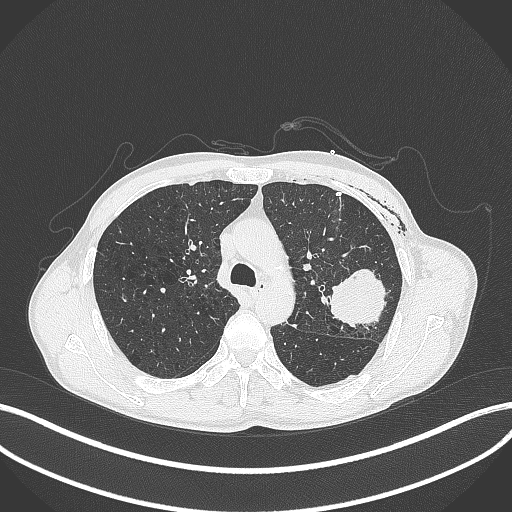
Chest CT, one axial slice; position 280 of 457 along the scan axis; reconstruction kernel B70f; 120 kVp; lung window (W 1500 / L -600 HU); 512 × 512 image matrix, field of view 400 × 400 mm. Male patient, age 58 years. Case-level facts recorded for this patient, not image findings: clinical TNM (as recorded): T3 N0 M0.
Annotated regions visible in this slice (rectangle marked by the reading radiologist):
- lung tumour (recorded histology: adenocarcinoma): bounding box (x1, y1, x2, y2) in pixels: (327, 264, 390, 328)